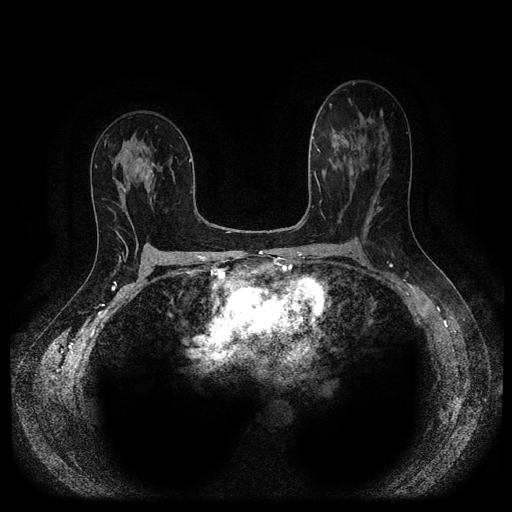
Breast MRI (dynamic contrast-enhanced, multi-phase), one axial slice. Position 57 of 116 along the scan axis. Dynamic contrast-enhanced series, time point 2 of 5 at this slice position (early post-contrast). 1.5 T. TE 2.6 ms, TR 5.3 ms. 2.2 mm slice thickness. 512 × 512 image matrix, field of view 340 × 340 mm. Patient: female, 50 years.
Annotated regions visible in this slice (semi-automatic segmentation, software-assisted and operator-edited):
- breast lesion (labelled 'tumour' in the annotation; benign lesions carry a separate 'benign' label): bounding box <133,147,155,178> (left, top, right, bottom; pixels)